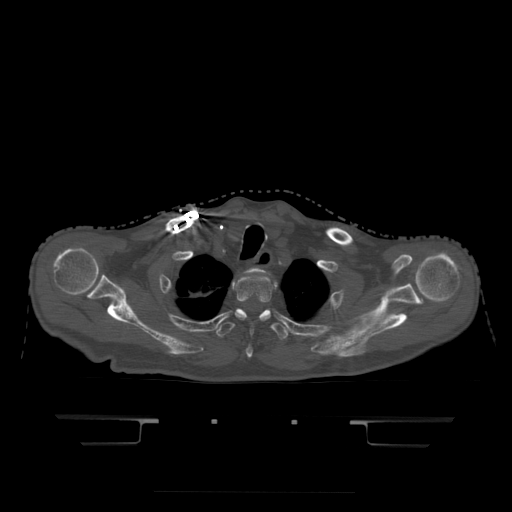
CT including the spine, one axial slice; slice 381 of 522 in the series (ordered by position); bone window (W 1800 / L 400 HU); 1.25 mm slice thickness; 512 × 512 image matrix, field of view 436 × 436 mm. Patient age 68 years. From the clinical record (not read from this slice): primary cancer: urothelial.
Outlined on this slice (semi-automatic segmentation, software-assisted and operator-edited):
- T1 vertebra: bounding box (x1, y1, x2, y2) in pixels: (245, 269, 266, 273)
- T2 vertebra: (236, 275, 272, 358)
- T3 vertebra: (216, 309, 288, 340)